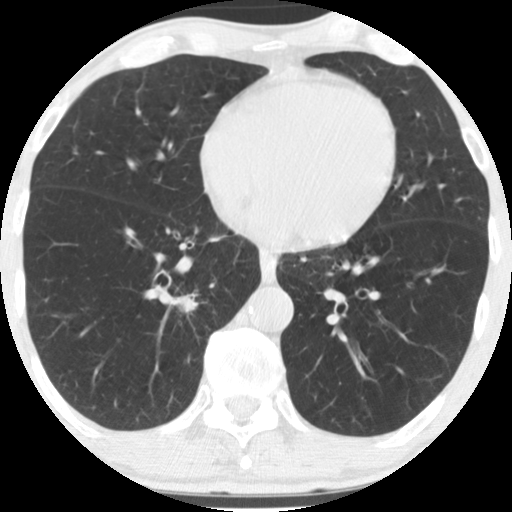
Low-dose screening chest CT, one axial slice; slice 60 of 170 in the series (ordered by position); reconstruction kernel STANDARD; 120 kVp; lung window (W 1500 / L -600 HU); 2.5 mm slice thickness; 512 × 512 image matrix, field of view 290 × 290 mm.
Structures marked on this image (expert manual segmentation):
- lesion 1 (tumor, lower lobe of right lung): bounding box (x1, y1, x2, y2) in pixels: (178, 297, 196, 311)